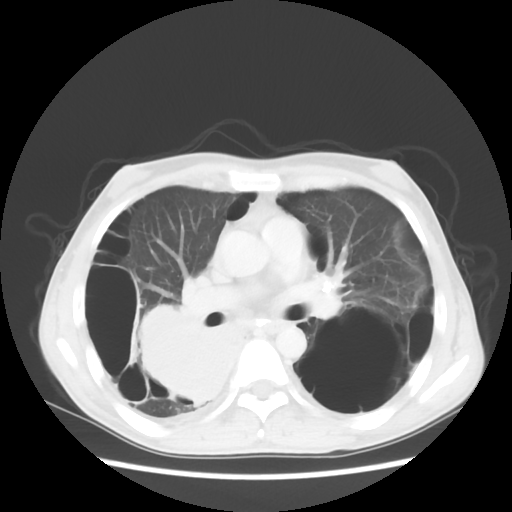
Chest CT, one axial slice. Position 30 of 56 along the scan axis. Reconstruction kernel STANDARD. 140 kVp. Lung window (W 1500 / L -600 HU). 5 mm slice thickness. 512 × 512 image matrix, field of view 351 × 351 mm. Male patient, age 41 years. Case-level facts recorded for this patient, not image findings: clinical TNM (as recorded): T4 N0 M1a; histopathological grade: G3.
Annotated regions visible in this slice (rectangle marked by the reading radiologist):
- lung tumour (recorded histology: large cell carcinoma): bounding box <133,300,248,404> (left, top, right, bottom; pixels)